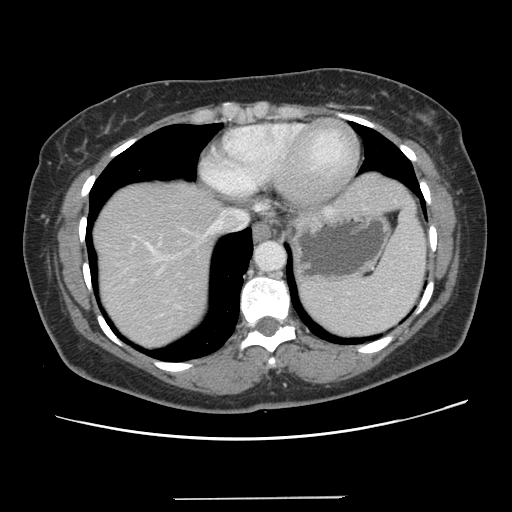
Contrast-enhanced abdominal CT, one axial slice; slice 117 of 141 in the series (ordered by position); intravenous contrast given; soft-tissue window (W 400 / L 40 HU); 2.5 mm slice thickness; 512 × 512 image matrix, field of view 366 × 366 mm. Female patient, age 53 years. Case-level facts recorded for this patient, not image findings: diagnosis: colorectal cancer liver metastases, imaged before liver resection; multiple liver metastases: no; largest metastasis: 14.5 cm; disease in both lobes: yes.
Structures marked on this image (manually delineated by an expert):
- hepatic veins: bounding box (x1, y1, x2, y2) in pixels: (114, 209, 247, 278)
- liver: (93, 173, 410, 349)
- planned liver remnant (the part of the liver to remain after resection): (93, 213, 218, 348)